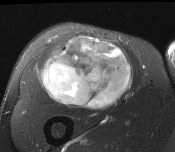
MRI of an extremity soft-tissue mass, one axial slice. T2-weighted fat-saturated. MR volume resampled by the dataset authors to the PET/CT grid (not the native acquisition matrix). 3.27 mm slice thickness. 175 × 152 image matrix, field of view 171 × 148 mm. Male patient. Case-level facts recorded for this patient, not image findings: histological type: pleiomorphic leiomyosarcoma; grade: intermediate; site of the primary tumour: right thigh.
Annotated regions visible in this slice (expert contour drawn on MRI and transferred to this co-registered scan by the dataset authors):
- gross tumour volume including surrounding oedema: bounding box (x1, y1, x2, y2) in pixels: (42, 37, 132, 110)
- gross tumour volume (mass): (44, 38, 132, 110)